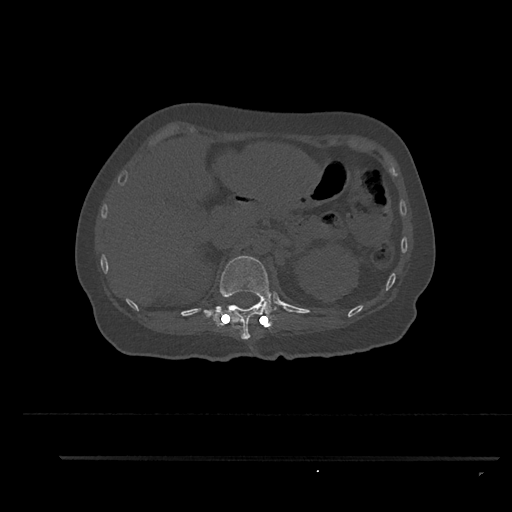
CT including the spine, one axial slice; slice 255 of 797 in the series (ordered by position); 120 kVp; bone window (W 1800 / L 400 HU); 0.5 mm slice thickness; 512 × 512 image matrix, field of view 408 × 408 mm. Patient: female, 44 years. From the clinical record (not read from this slice): primary cancer: renal.
Outlined on this slice (semi-automatic segmentation, software-assisted and operator-edited):
- T12 vertebra: bounding box [x1, y1, x2, y2] px = [203, 256, 277, 340]